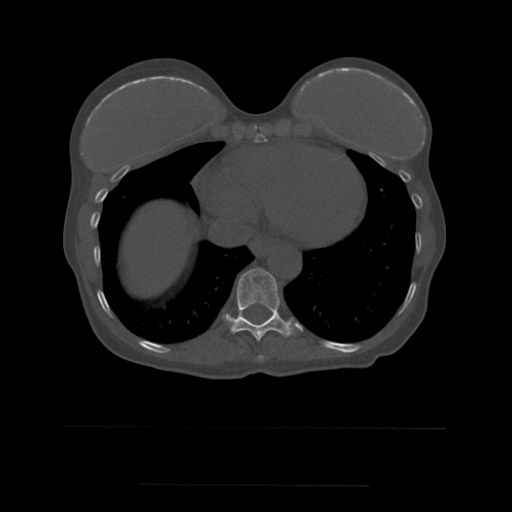
CT including the spine, one axial slice. Slice 302 of 544 in the series (ordered by position). Bone window (W 1800 / L 400 HU). 512 × 512 image matrix, field of view 350 × 350 mm. Patient age 58 years. From the clinical record (not read from this slice): primary cancer: lung.
Structures marked on this image (semi-automatically segmented with operator editing):
- T10 vertebra: bounding box <226,269,294,342> (left, top, right, bottom; pixels)
- T9 vertebra: <258,356,263,359>